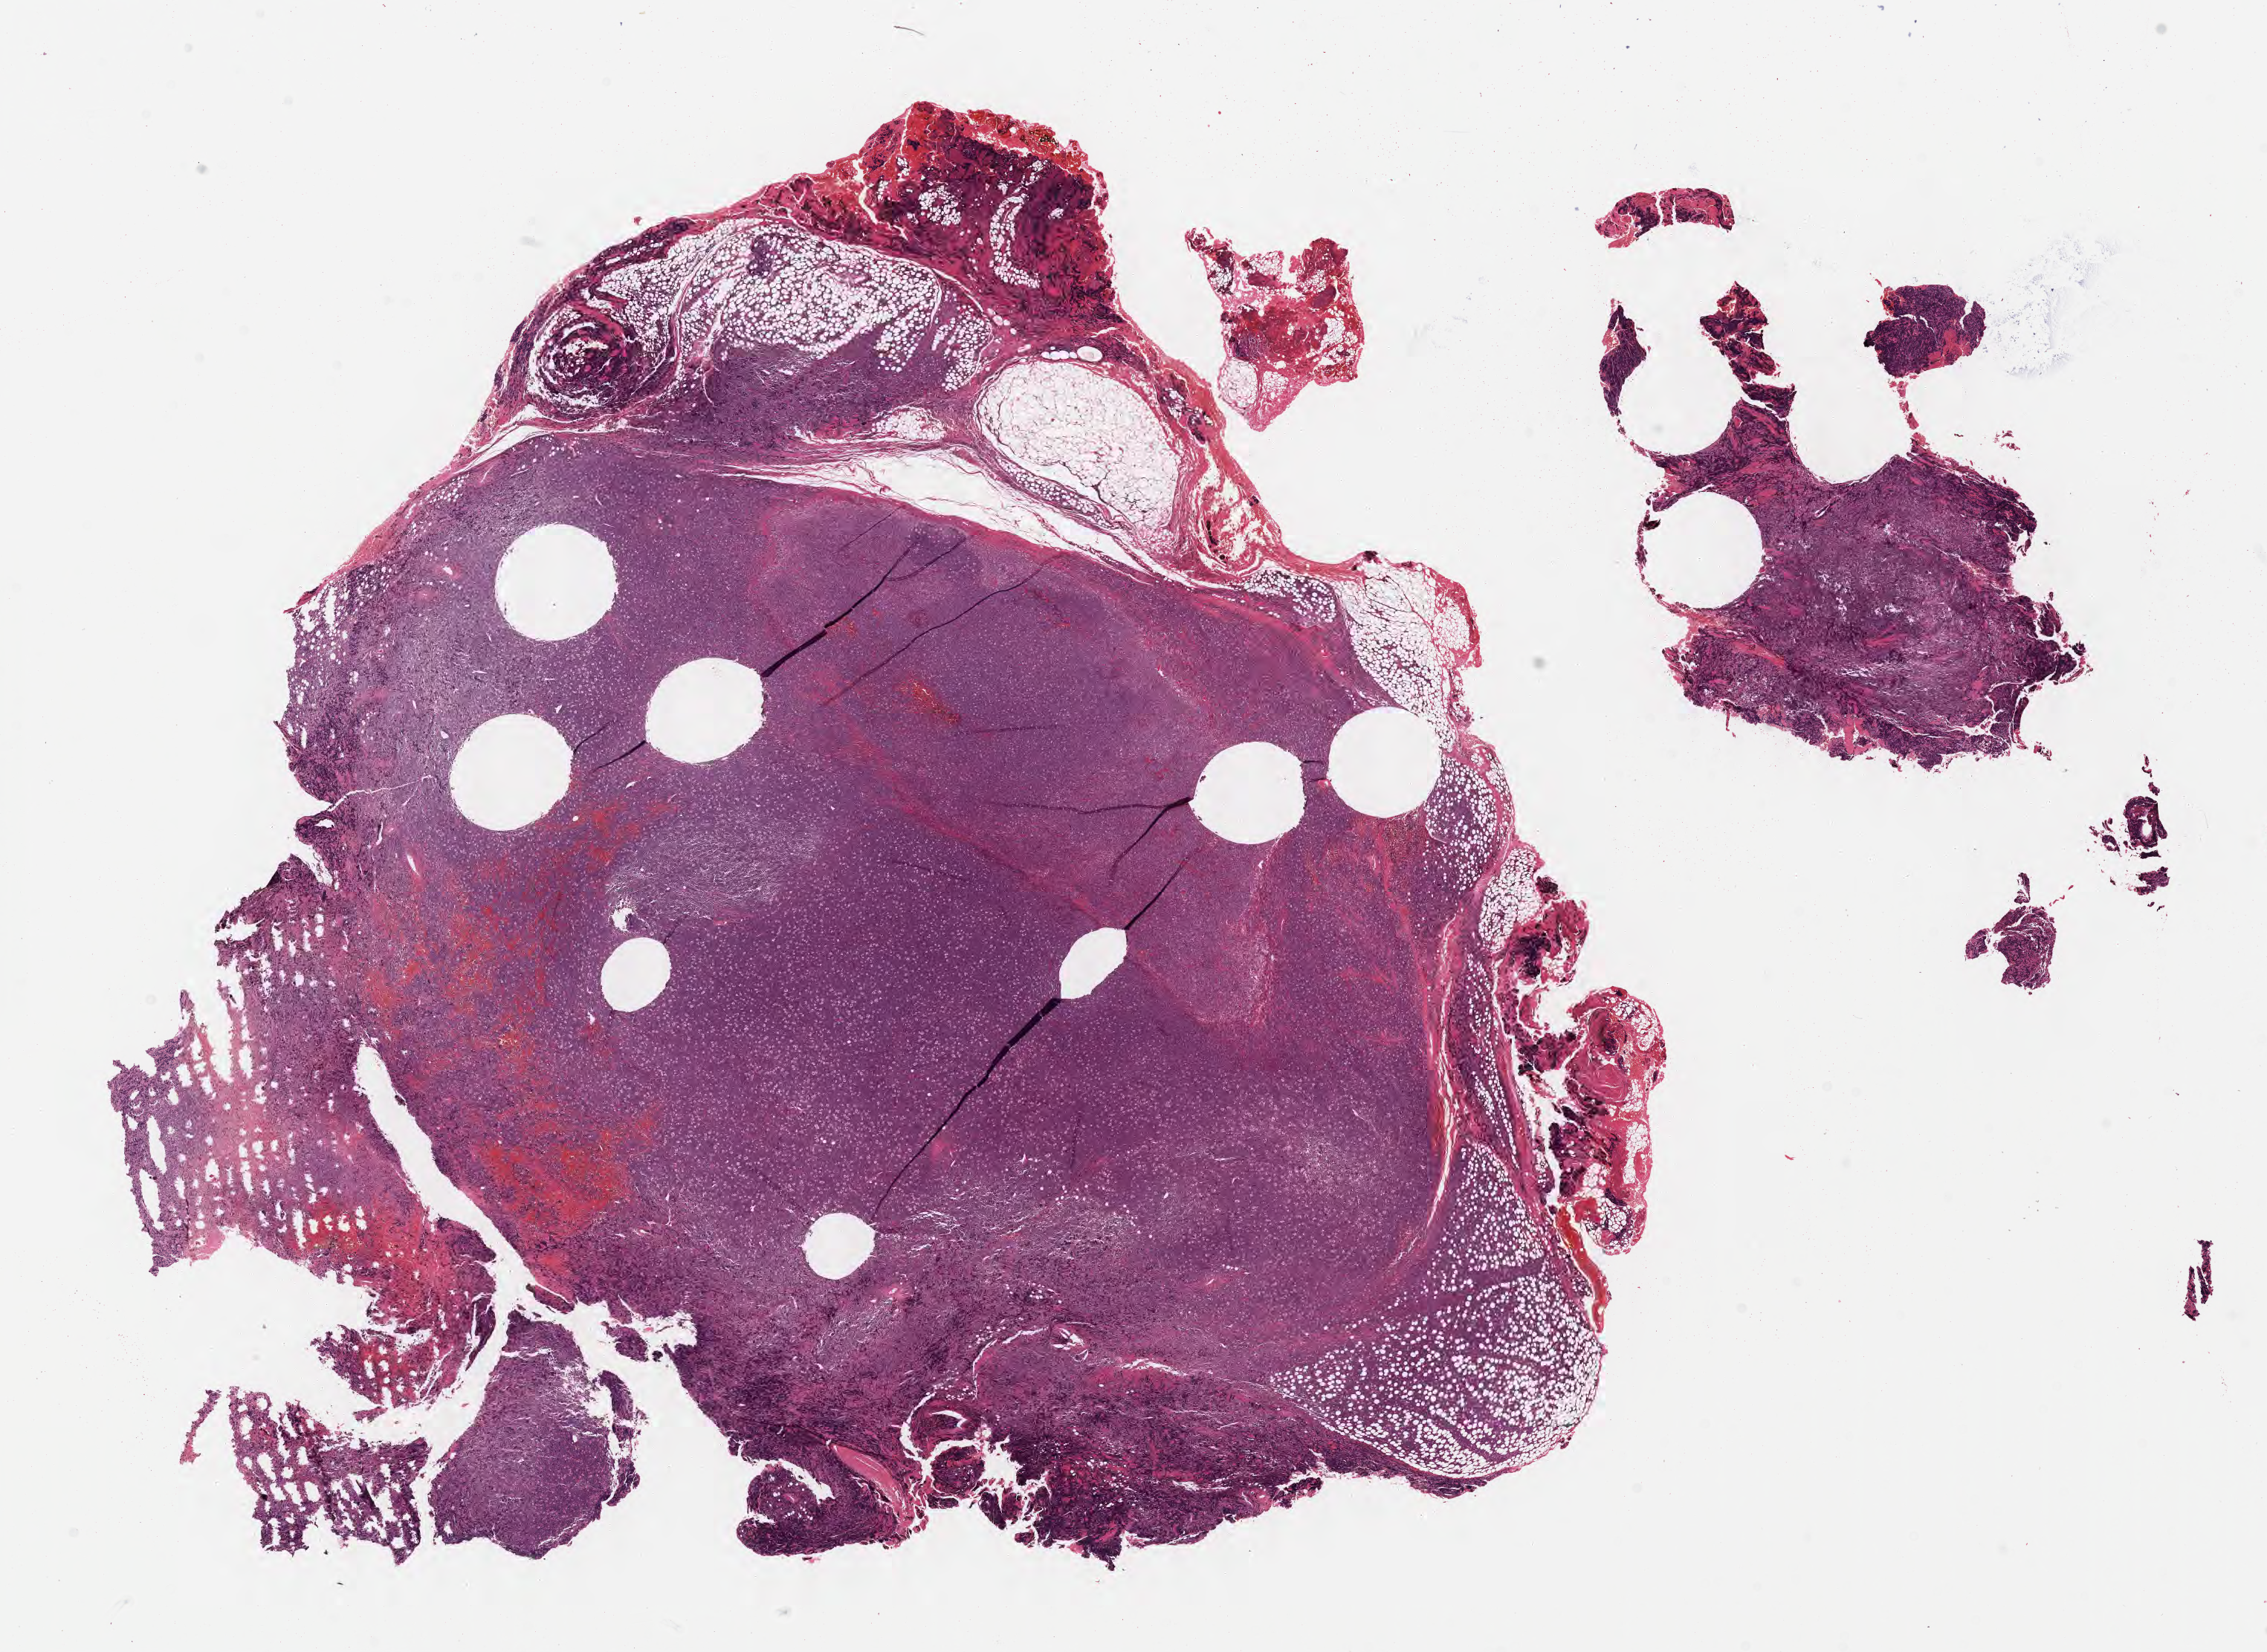
Whole-slide image, haematoxylin and eosin stain — a low-resolution overview of the entire scanned area, about 24.6 x 18.0 mm. Patient: male, age 40 years. Composition of this section per pathologist review: tumor cells 80%, tumor nuclei 90%, stromal cells 10%, necrosis 5%, normal cells 5%. Infiltration values recorded for this section: lymphocyte infiltration 20%, monocyte infiltration 40%, neutrophil infiltration 5%.
• specimen: formalin-fixed paraffin-embedded section; primary tumor